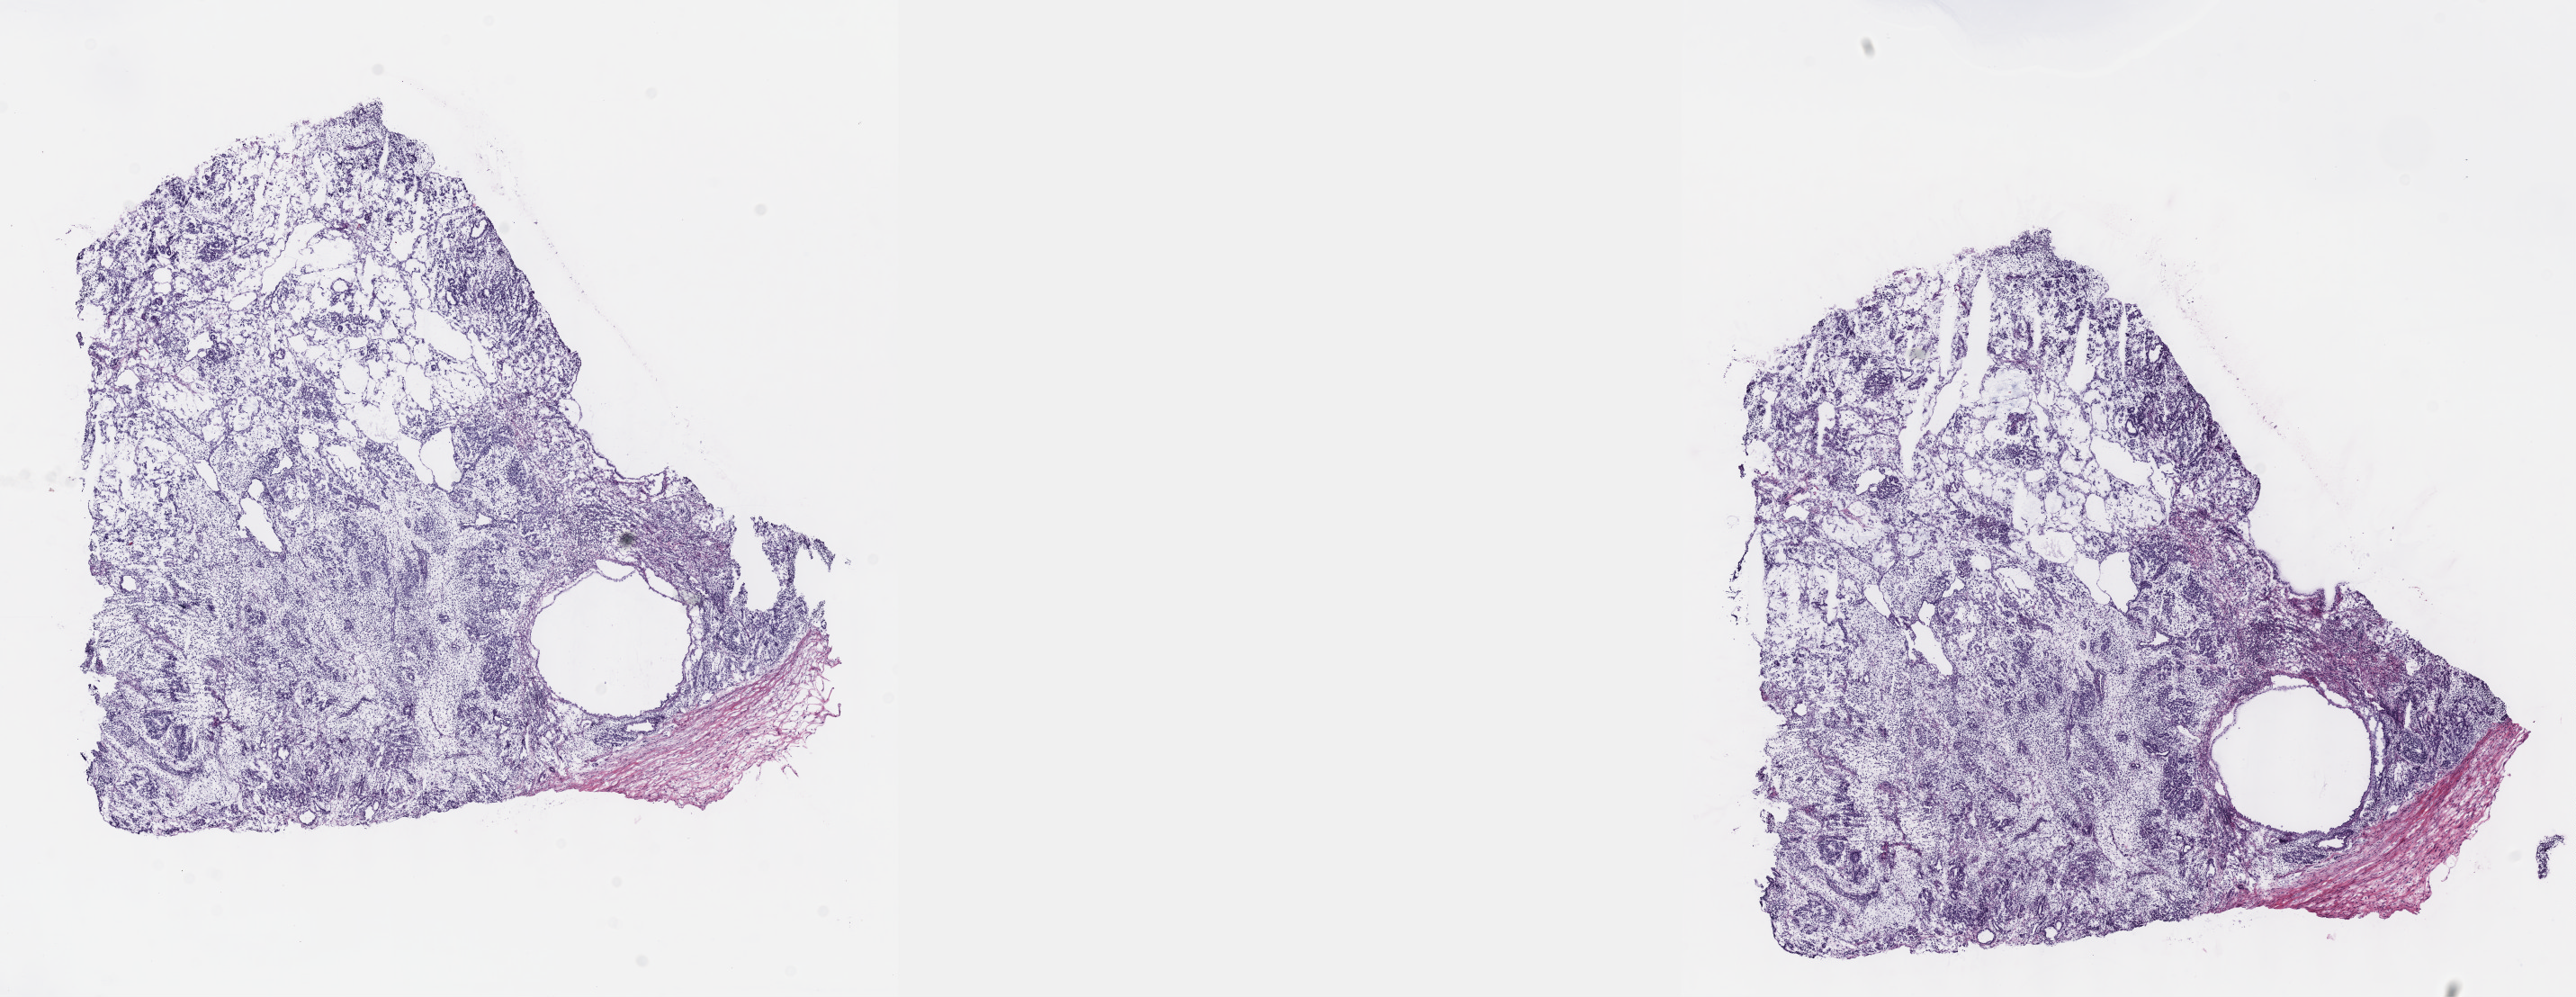
H&E-stained whole-slide image — low-resolution overview of the scanned area, about 23.1 x 9.0 mm (acquisition: 40x scan). Patient sex: male. Pathologist review of this section (percent, as recorded): tumour cells 80%, tumour nuclei 80%, normal cells 0%, stromal cells 20%, necrosis 0%. Infiltration values recorded for this section: lymphocyte infiltration 40%, monocyte infiltration 20%, neutrophil infiltration 20%.
Specimen: frozen section from the top of the tissue portion; sample: primary tumour, testis.